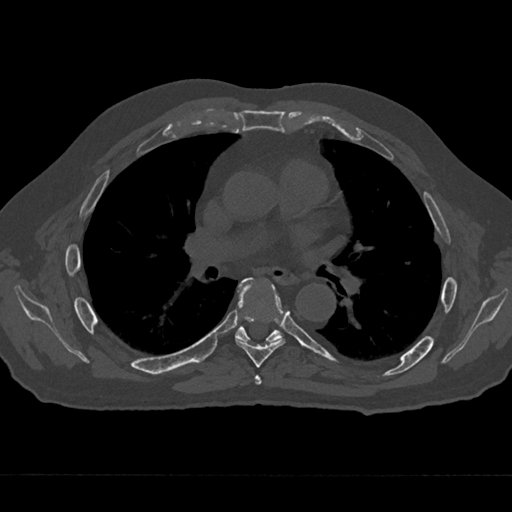
CT including the spine, one axial slice; bone window (W 1800 / L 400 HU); 0.5 mm slice thickness; 512 × 512 image matrix, field of view 377 × 377 mm. Patient: male, 75 years. Case-level facts recorded for this patient, not image findings: primary cancer: renal.
Structures marked on this image (semi-automatically segmented with operator editing):
- T5 vertebra: bounding box [x1, y1, x2, y2] px = [255, 375, 262, 385]
- T6 vertebra: [235, 278, 286, 368]
- T7 vertebra: [235, 279, 283, 343]